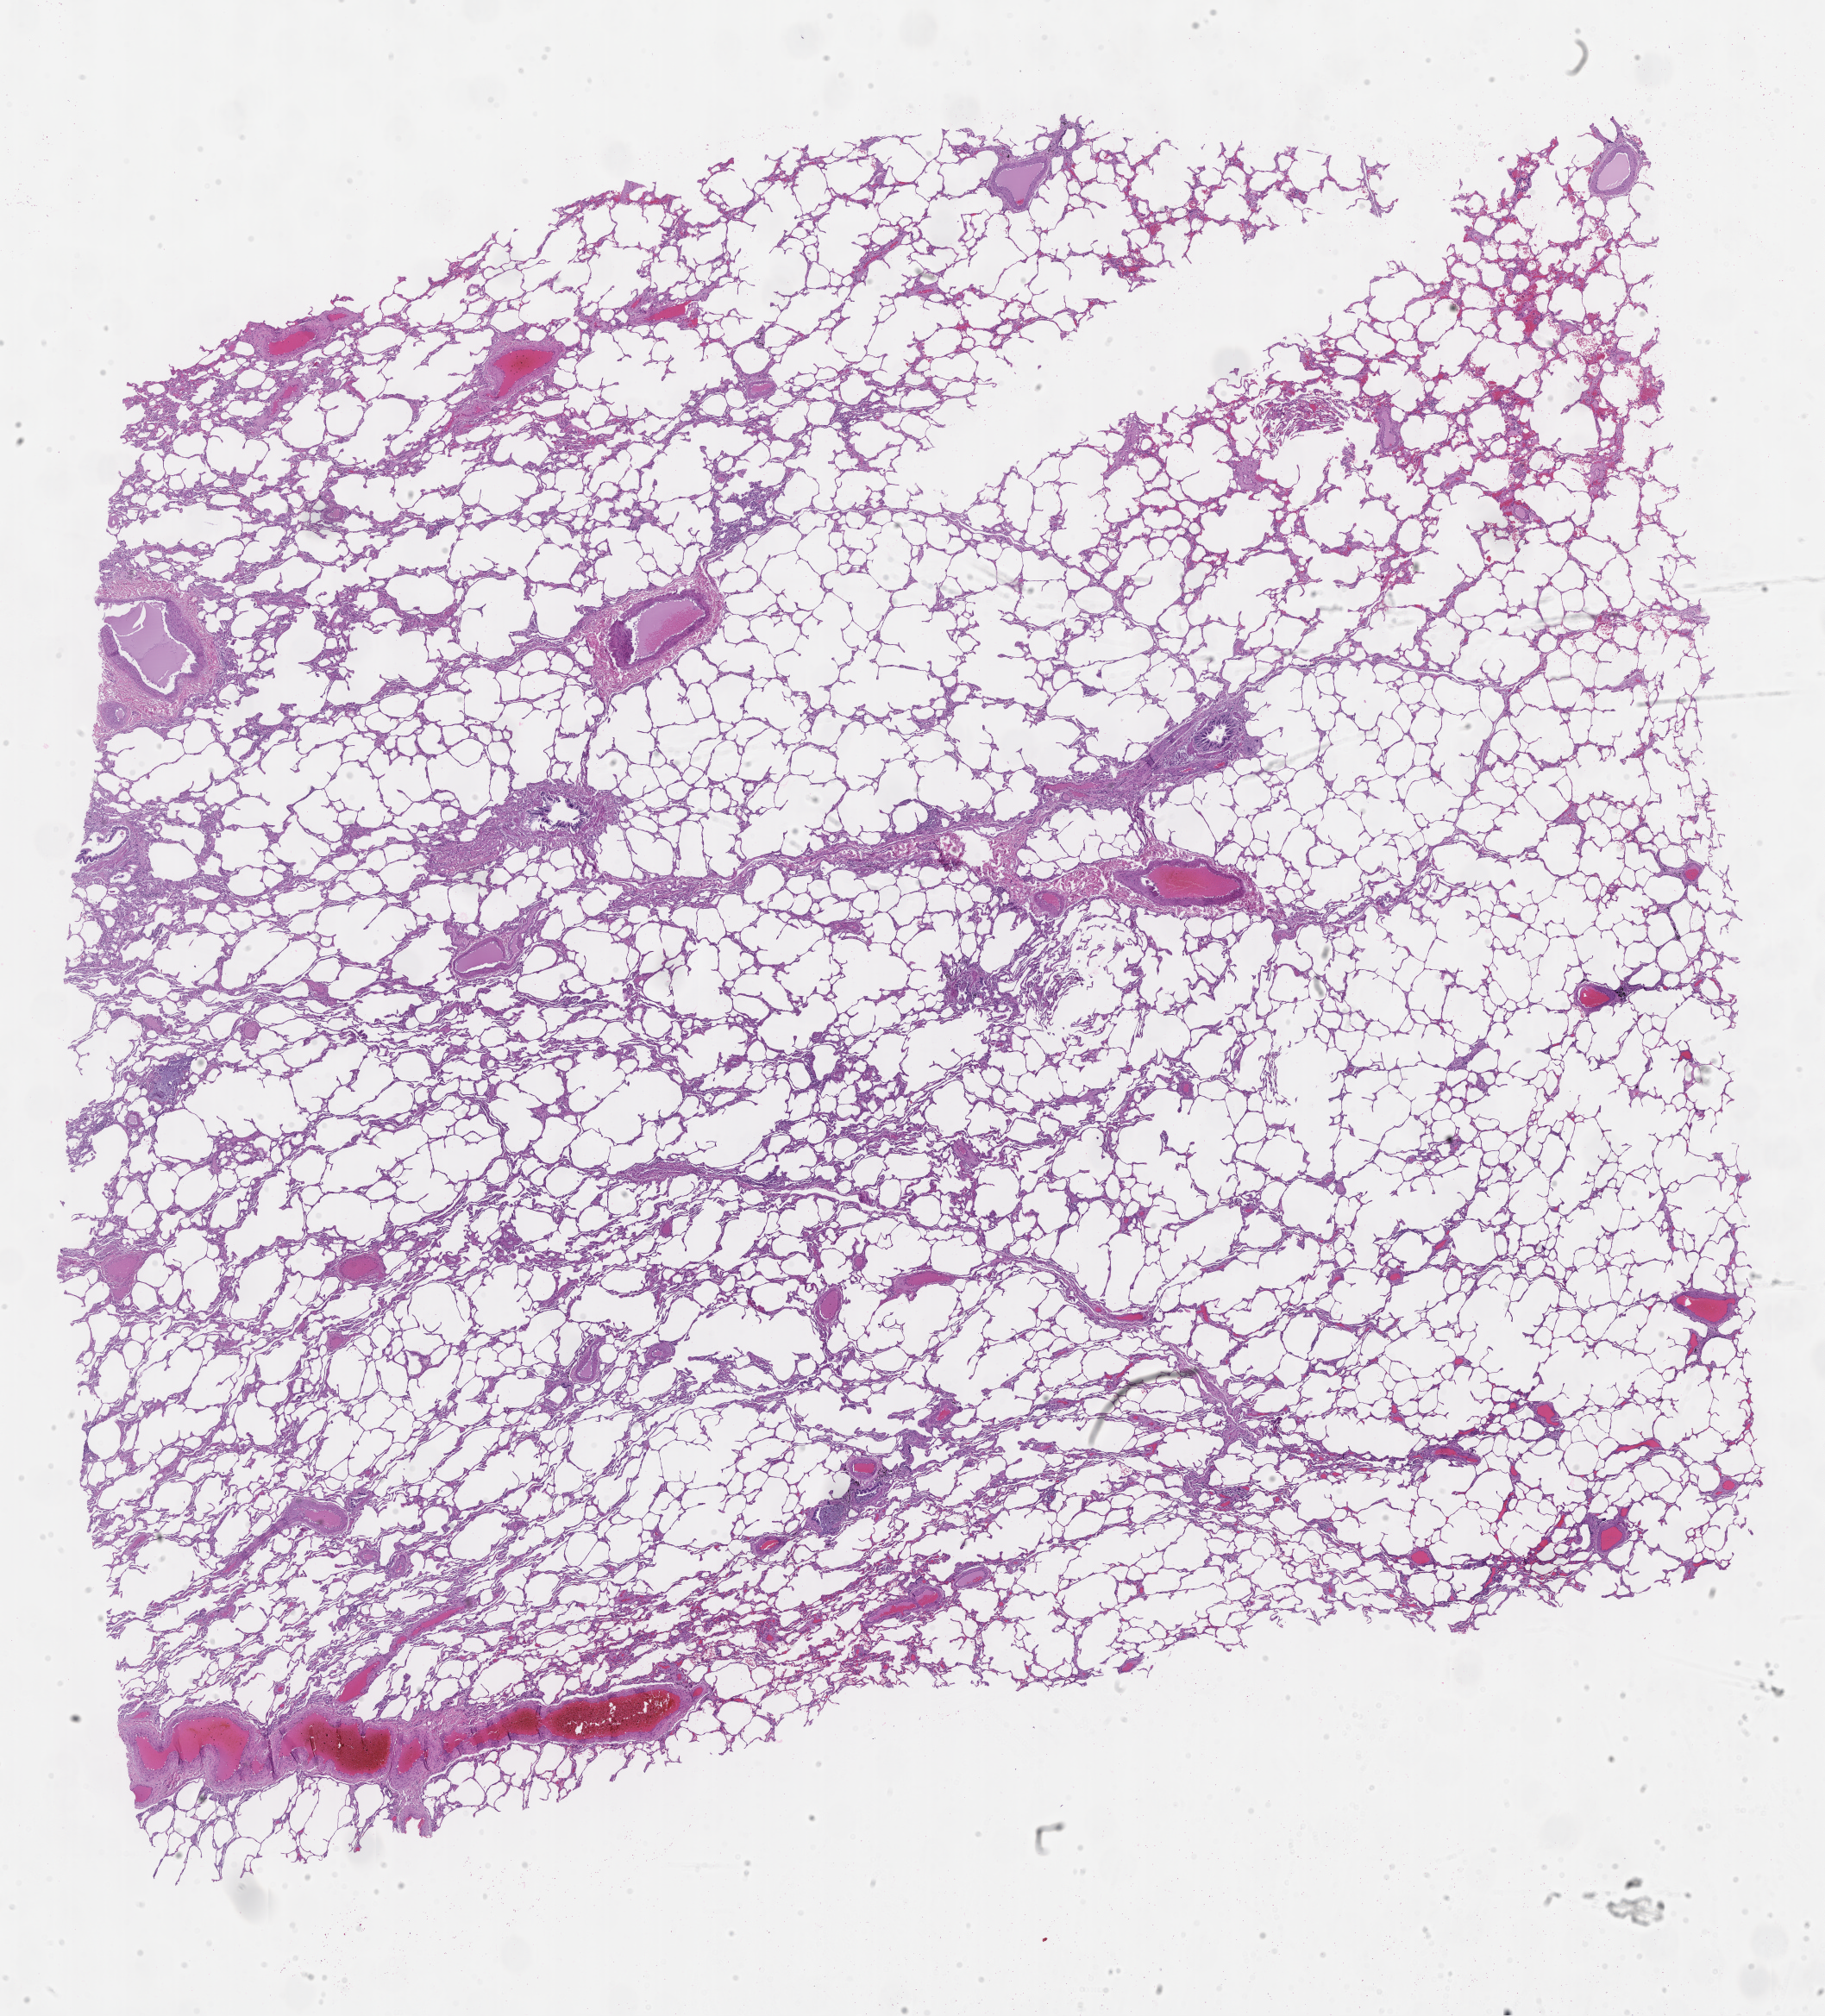
Whole-slide histology image, Hematoxylin and eosin (H&E) stained — whole scanned area (about 17.1 x 18.9 mm, slide scanned at 40x) shown as a low-resolution overview. Normal (non-tumour) tissue sample, sampled site: lung. 57-year-old male patient.
This section: normal (non-tumour) tissue from the same patient. Patient diagnosis: Adenocarcinoma, NOS.